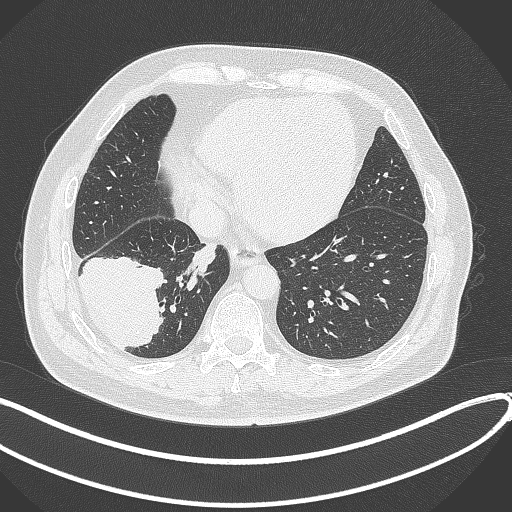
Chest CT, one axial slice; position 105 of 360 along the scan axis; 120 kVp; lung window (W 1500 / L -600 HU); 1 mm slice thickness; 512 × 512 image matrix, field of view 400 × 400 mm. Patient: male, 59 years.
Outlined on this slice (rectangle marked by the reading radiologist):
- lung tumour (recorded histology: adenocarcinoma): box from (x=80, y=257) to (x=167, y=350) px